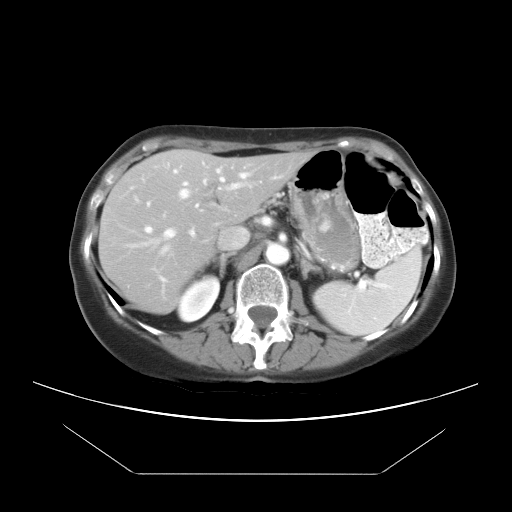
Contrast-enhanced abdominal CT, one axial slice. Position 14 of 21 along the scan axis. 120 kVp. Intravenous contrast given. Soft-tissue window (W 400 / L 40 HU). 512 × 512 image matrix. Female patient, age 72 years. Case-level facts recorded for this patient, not image findings: diagnosis: colorectal cancer liver metastases, imaged before liver resection; multiple liver metastases: yes; largest metastasis: 4 cm.
Outlined on this slice (expert manual segmentation):
- hepatic veins: box from (x=142, y=173) to (x=248, y=254) px
- liver: (x=100, y=151)–(x=309, y=313)
- planned liver remnant (the part of the liver to remain after resection): (x=100, y=151)–(x=309, y=280)
- portal vein (with intrahepatic branches): (x=144, y=183)–(x=241, y=280)